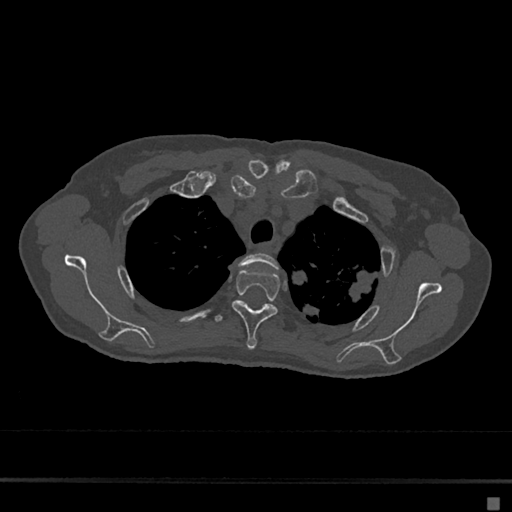
CT including the spine, one axial slice. Position 537 of 797 along the scan axis. Reconstruction kernel Br40s/3. 120 kVp. Bone window (W 1800 / L 400 HU). 0.5 mm slice thickness. 512 × 512 image matrix. Female patient, age 68 years. Case-level facts recorded for this patient, not image findings: primary cancer: renal.
Structures marked on this image (semi-automatic segmentation, software-assisted and operator-edited):
- T2 vertebra: bounding box <235,253,279,304> (left, top, right, bottom; pixels)
- T3 vertebra: <232,269,280,350>
- T4 vertebra: <214,306,265,323>